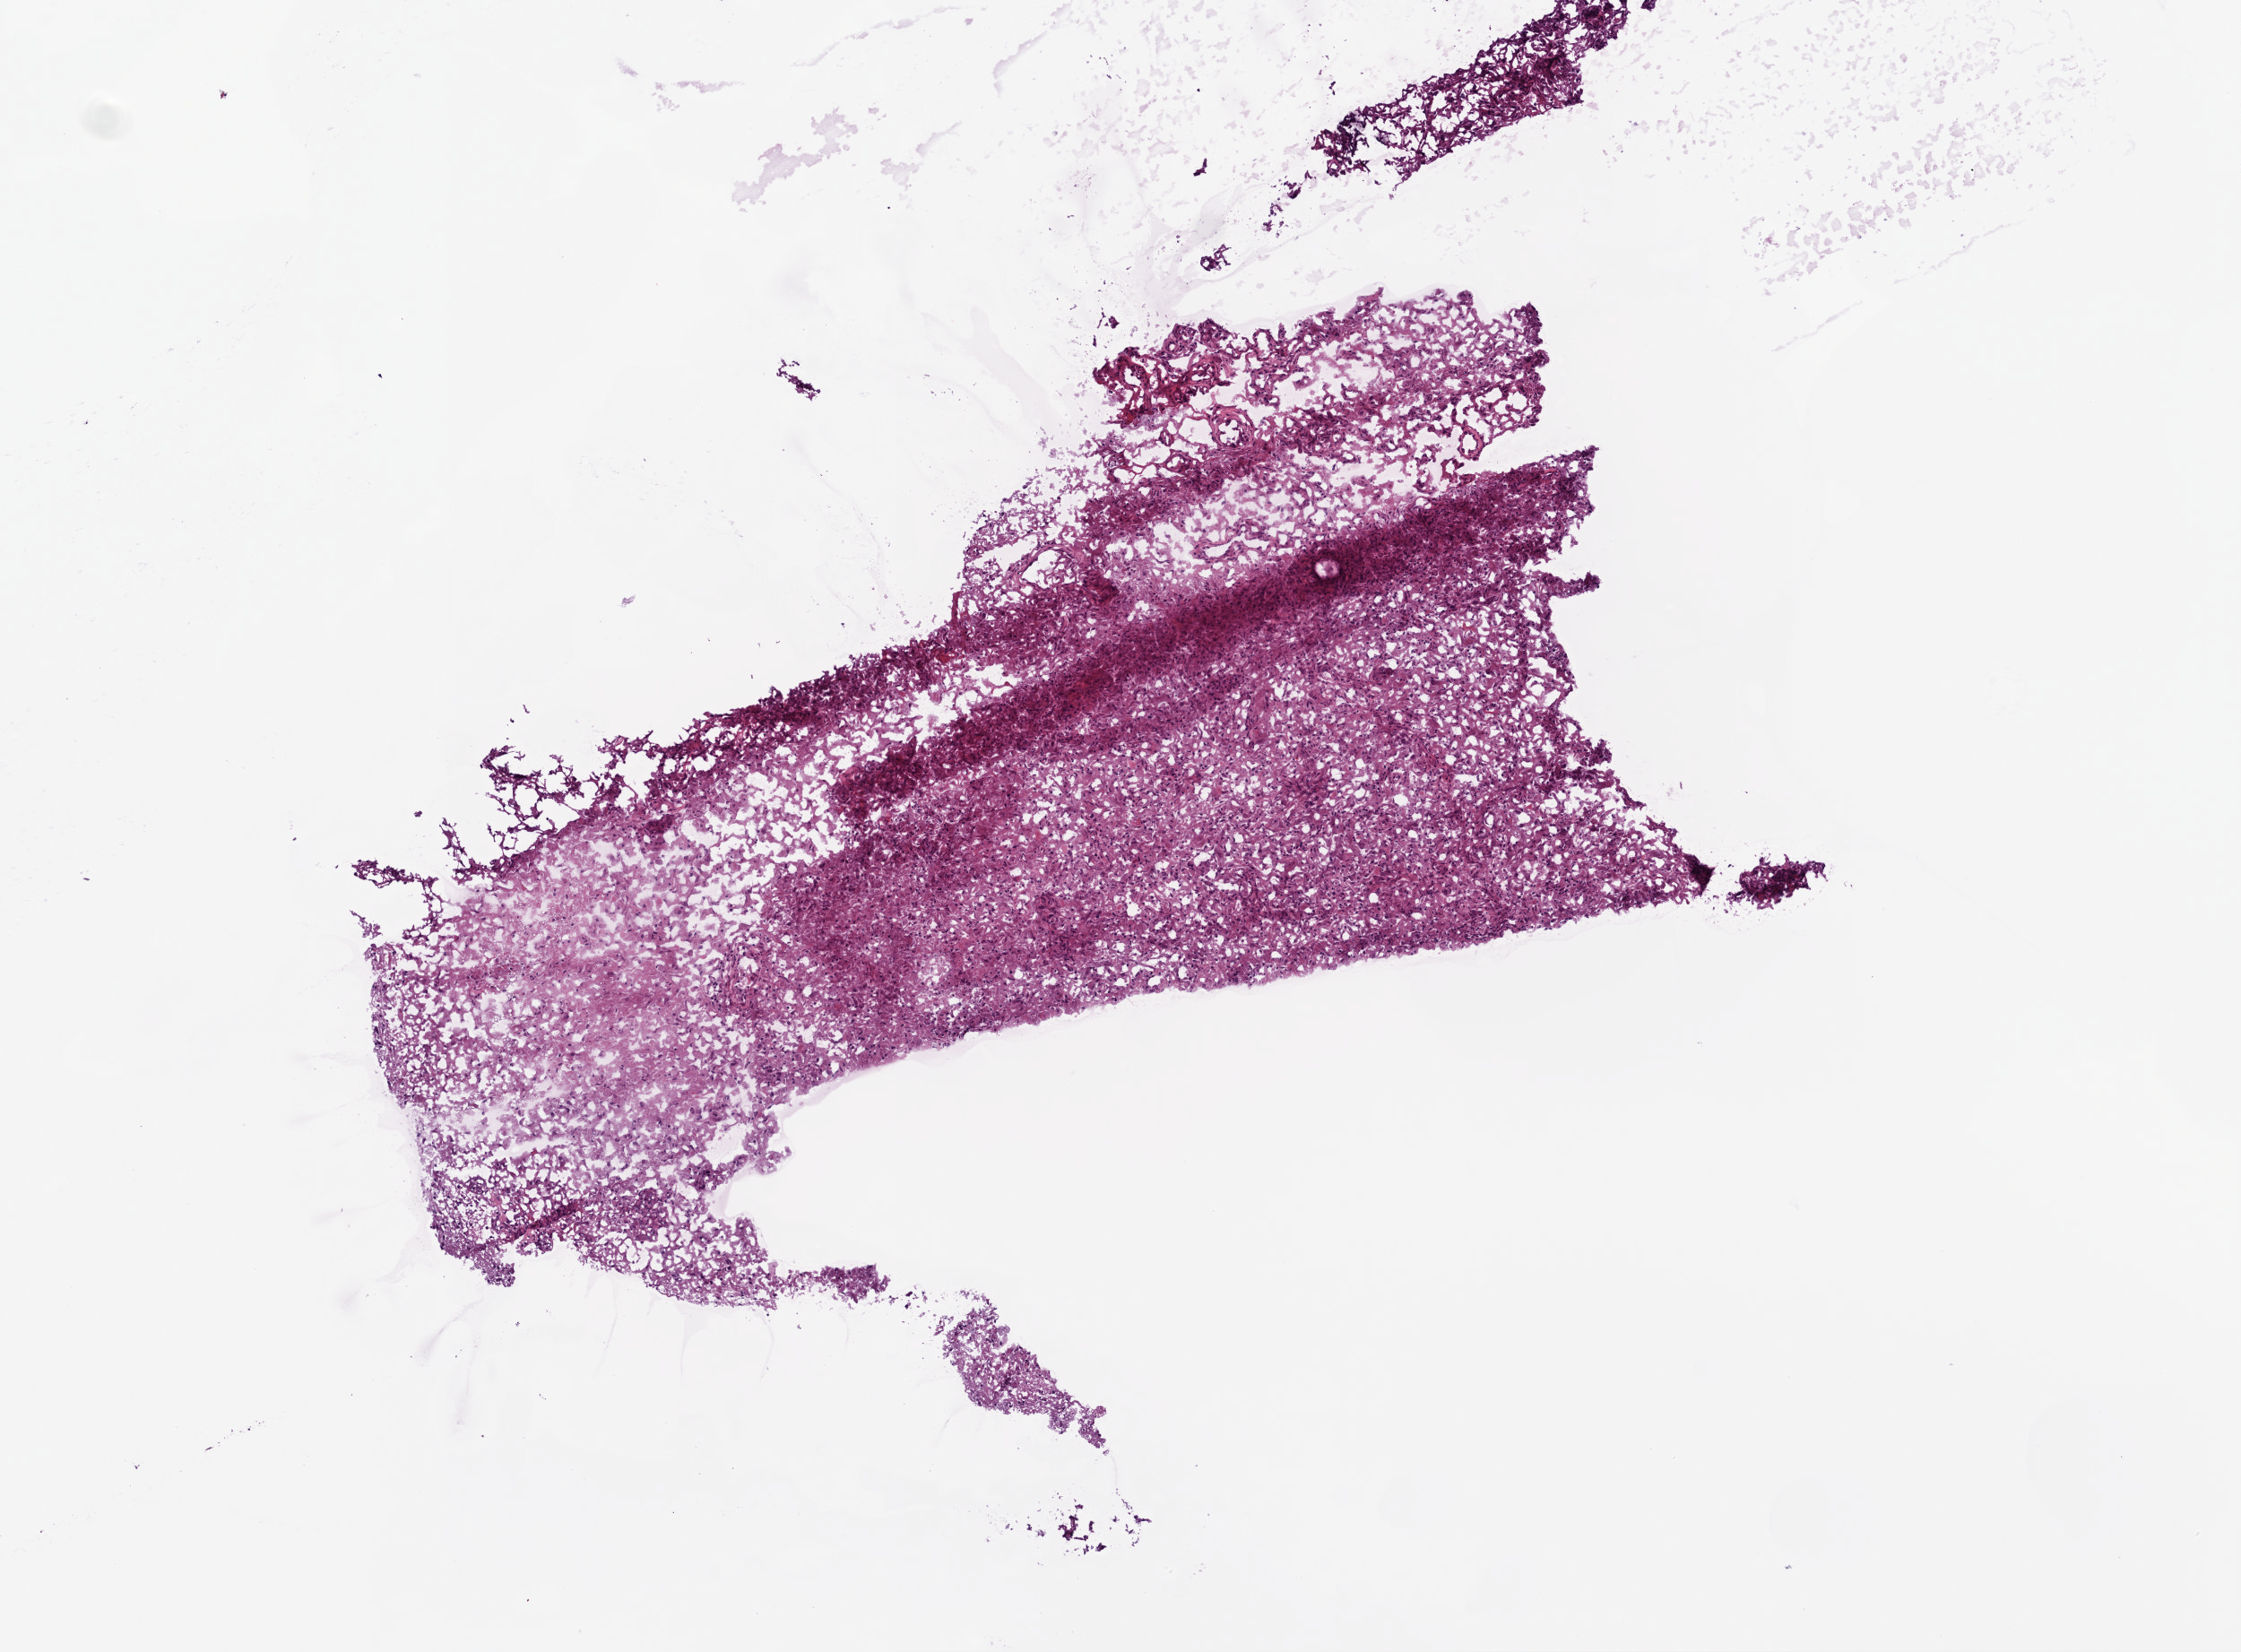
Digitized H&E-stained tissue section (whole slide), low-resolution overview of the scanned area, about 5.0 x 3.7 mm (acquisition: 20x scan); frozen section from the bottom of the tissue portion; primary tumour sample from the brain. Male patient; age at initial diagnosis 81 years. Pathologist review of this section (percent, as recorded): tumour cells 99%, tumour nuclei 85%, normal cells 0%, stromal cells 0%, necrosis 1%.
Diagnosis: Glioblastoma.